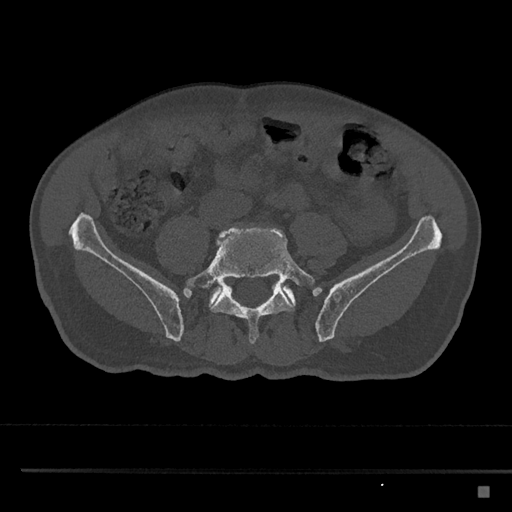
CT including the spine, one axial slice; slice 577 of 797 in the series (ordered by position); reconstruction kernel Br40s/3; bone window (W 1800 / L 400 HU); 0.5 mm slice thickness; 512 × 512 image matrix, field of view 391 × 391 mm. Patient: male, 59 years. Case-level facts recorded for this patient, not image findings: primary cancer: prostate.
Annotated regions visible in this slice (semi-automatic segmentation, software-assisted and operator-edited):
- L5 vertebra: bounding box (x1, y1, x2, y2) in pixels: (183, 225, 315, 344)